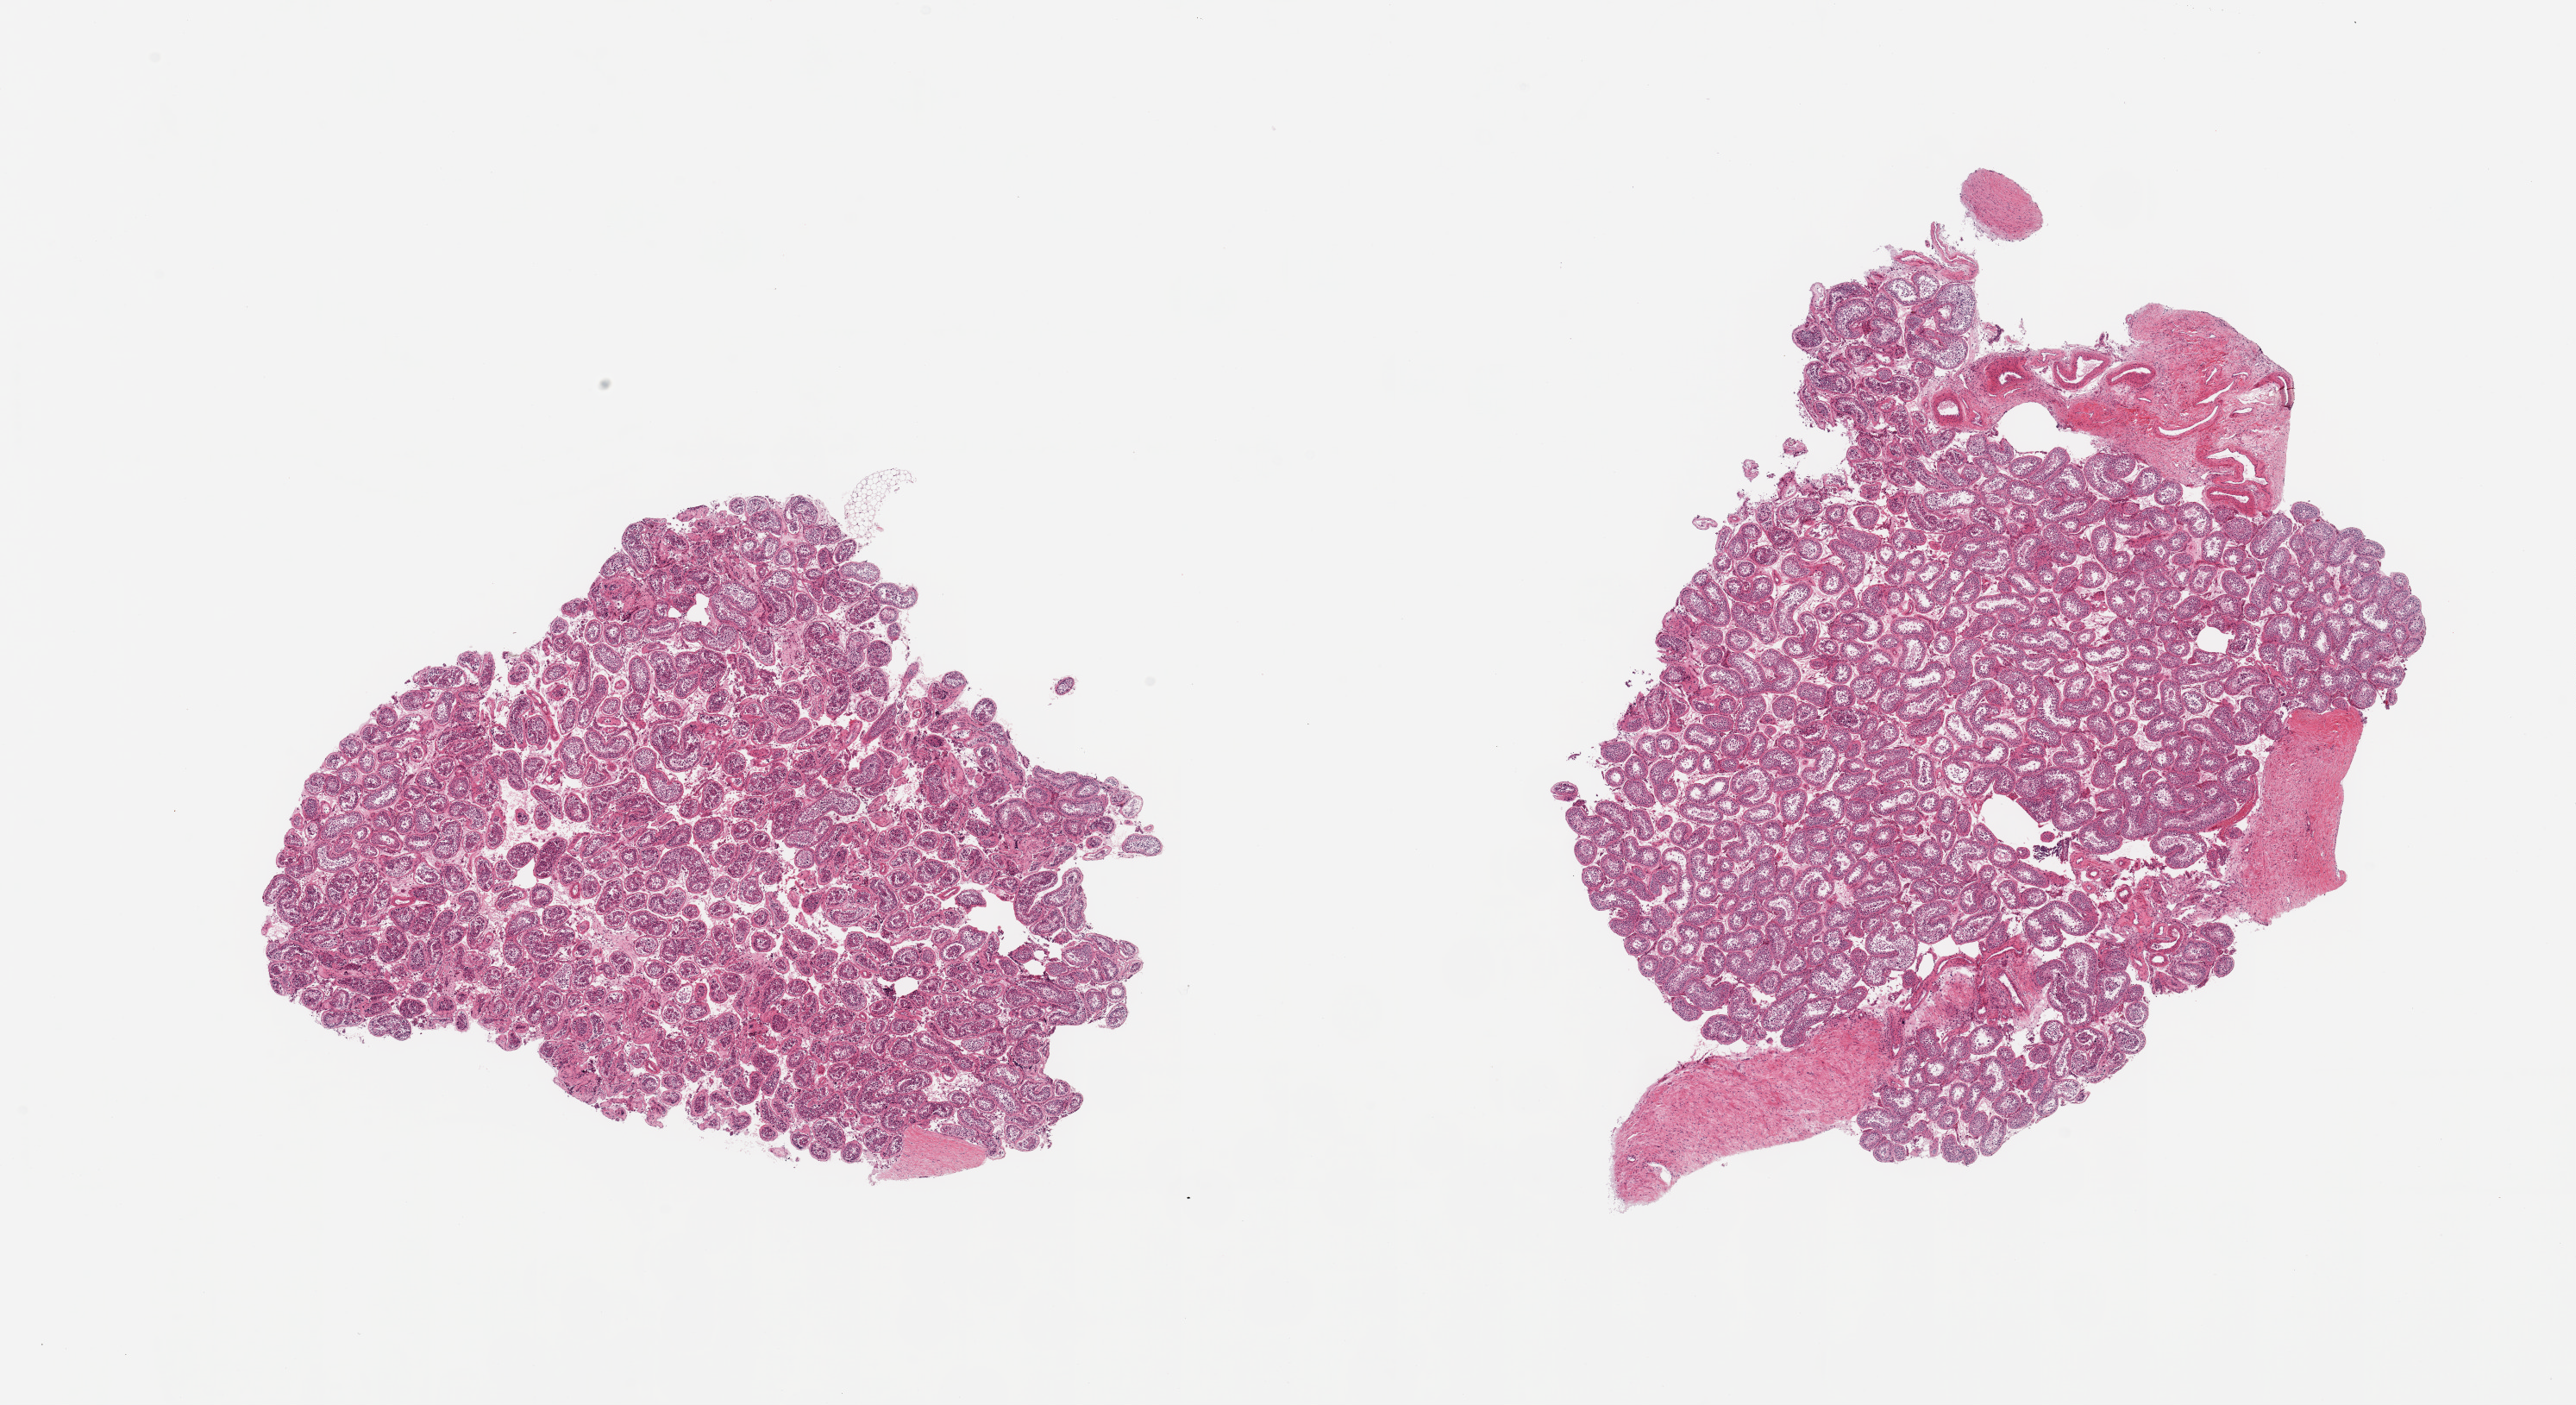
Haematoxylin and eosin whole-slide image, low-resolution overview of the scanned area, about 23.6 x 12.9 mm (slide scanned at 20x). PAXgene-fixed, paraffin-embedded tissue. Section of testis (target tissue). Tissue donor sample. Male donor.
Pathologist's review note for this sample: 2 pieces; autolysis varies from slight to moderate between the 2 pieces.